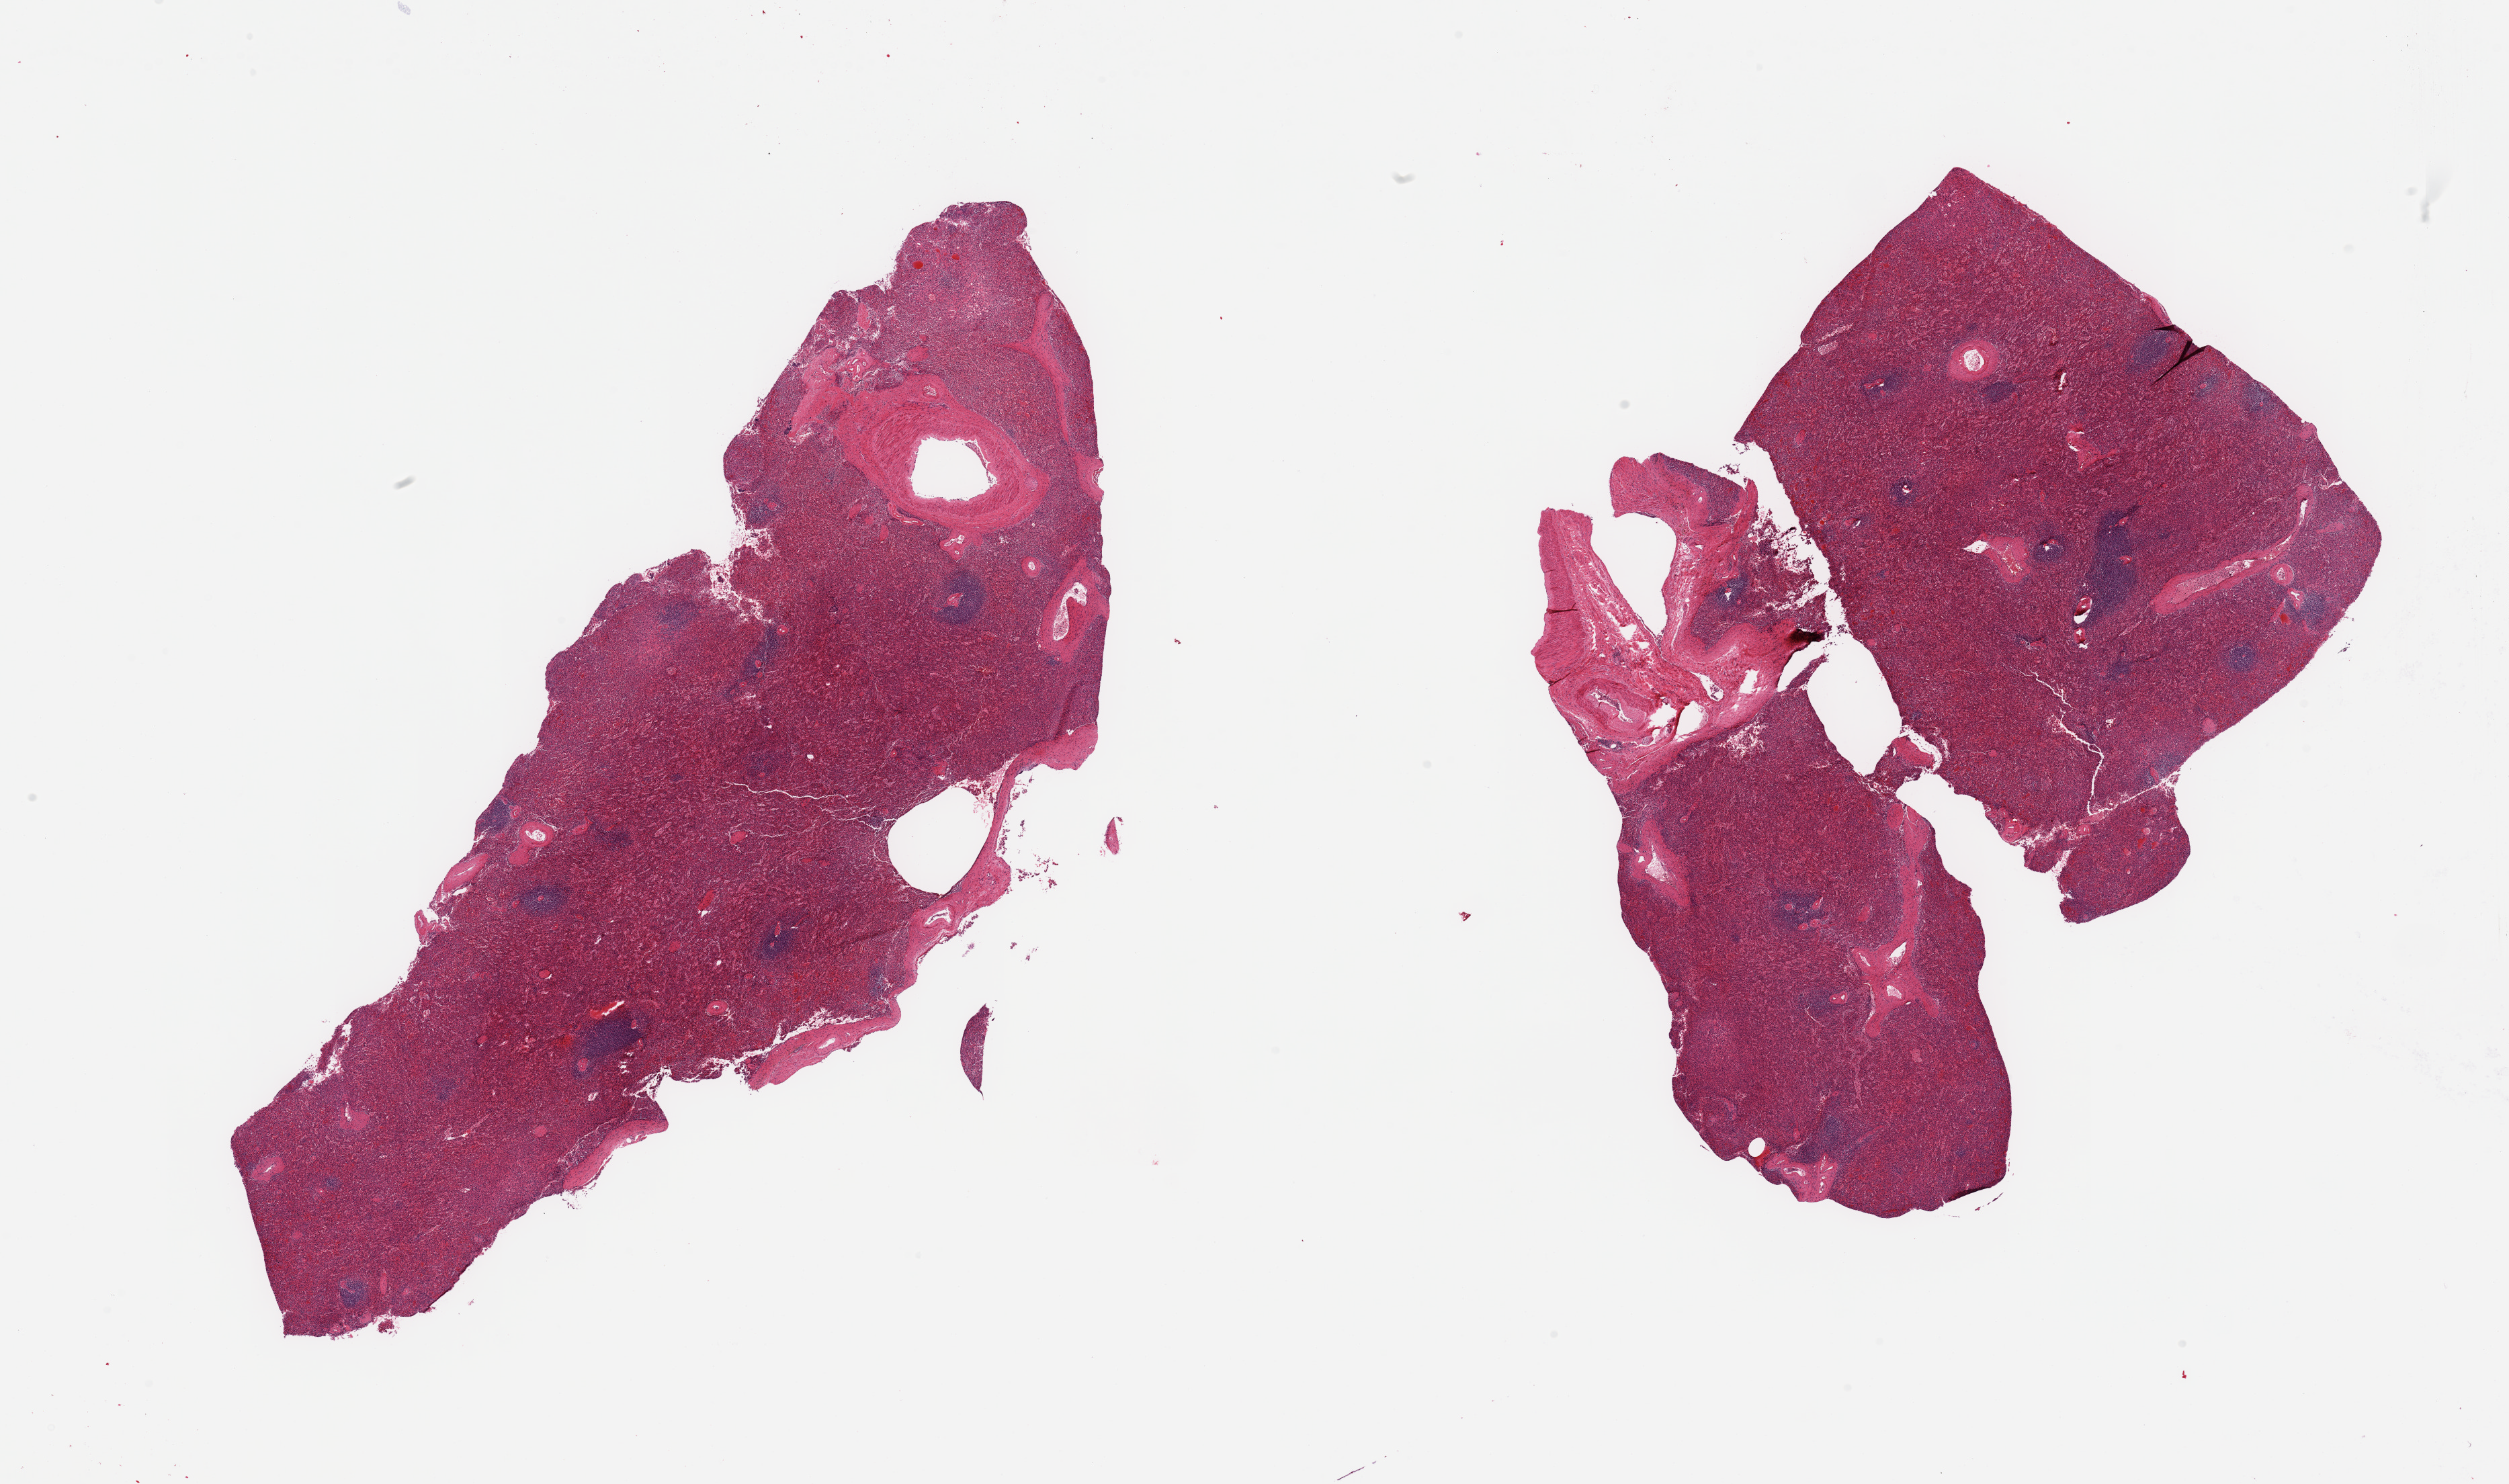
Digitized H&E-stained section, shown as a low-resolution overview of the whole scanned area (about 29.5 x 17.5 mm), PAXgene-fixed paraffin-embedded (PFPE) section, section of spleen (target tissue), donor tissue sample. Donor sex: male.
* review note (as recorded): branch